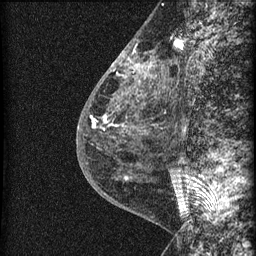
Breast MRI (dynamic contrast-enhanced), one sagittal slice; slice 24 of 60 in the series (ordered by position); dynamic contrast-enhanced series, image 2 of 3 at this slice position (ordered by acquisition); 1.5 T; TE 4.2 ms, TR 22.7 ms; 1.5 mm slice thickness; 256 × 256 image matrix, field of view 180 × 180 mm. Patient: female, 48 years. Case-level facts recorded for this patient, not image findings: setting: breast cancer imaged before/during neoadjuvant chemotherapy; receptor status: triple-negative.
Annotated regions visible in this slice (semi-automatic segmentation, software-assisted and operator-edited):
- analysis volume of interest (the breast-tissue region the enhancement analysis was run in; not a lesion): bounding box [x1, y1, x2, y2] px = [115, 34, 169, 162]
- tumour enhancement mask (voxels above the 90 % enhancement threshold inside the analysis volume of interest): [126, 59, 152, 78]